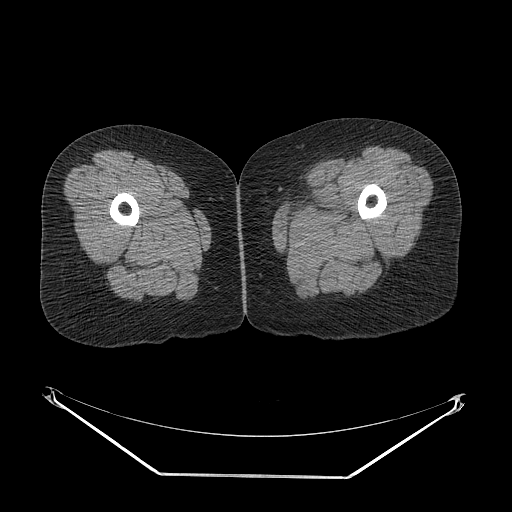
CT of an extremity soft-tissue mass (from a PET/CT study), one axial slice. Position 5 of 267 along the scan axis. Reconstruction kernel STANDARD. Soft-tissue window (W 400 / L 40 HU). 3.75 mm slice thickness. 512 × 512 image matrix, field of view 500 × 500 mm. Female patient. From the clinical record (not read from this slice): histological type: myxofibrosarcoma; grade: intermediate; site of the primary tumour: left thigh.
Outlined on this slice (expert contour drawn on MRI and transferred to this co-registered scan by the dataset authors):
- gross tumour volume including surrounding oedema: bounding box <288,201,348,234> (left, top, right, bottom; pixels)